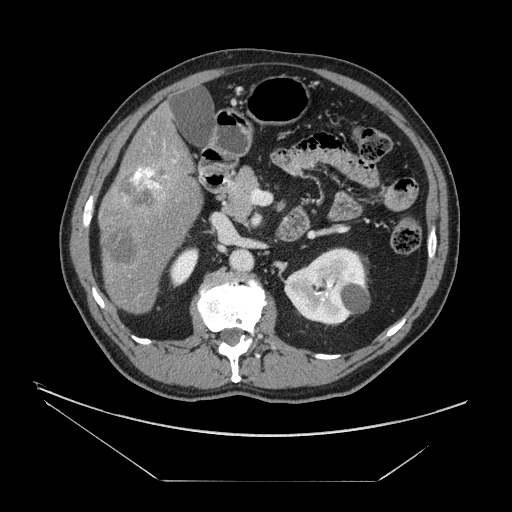
Contrast-enhanced abdominal CT, one axial slice. Position 69 of 161 along the scan axis. Intravenous contrast given. Soft-tissue window (W 400 / L 40 HU). 2.5 mm slice thickness. 512 × 512 image matrix, field of view 440 × 440 mm. Male patient, age 65 years. Case-level facts recorded for this patient, not image findings: diagnosis: colorectal cancer liver metastases, imaged before liver resection; multiple liver metastases: yes; largest metastasis: 4.2 cm; disease in both lobes: yes.
Annotated regions visible in this slice (outlined manually by an expert reader):
- liver: bounding box <101,108,202,314> (left, top, right, bottom; pixels)
- portal vein (with intrahepatic branches): <132,161,175,190>
- liver metastasis: <105,229,139,267>
- liver metastasis: <118,167,171,209>